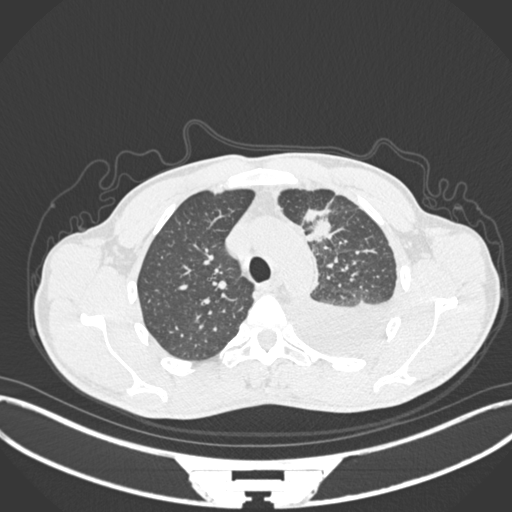
Chest CT, one axial slice; slice 166 of 244 in the series (ordered by position); reconstruction kernel B30f; 120 kVp; lung window (W 1500 / L -600 HU); 1 mm slice thickness; 512 × 512 image matrix, field of view 400 × 400 mm. Male patient, age 49 years. Case-level facts recorded for this patient, not image findings: clinical TNM (as recorded): T1c N1 M1.
Annotated regions visible in this slice (bounding box drawn by a radiologist):
- lung tumour (recorded histology: adenocarcinoma): bounding box <301,207,337,242> (left, top, right, bottom; pixels)